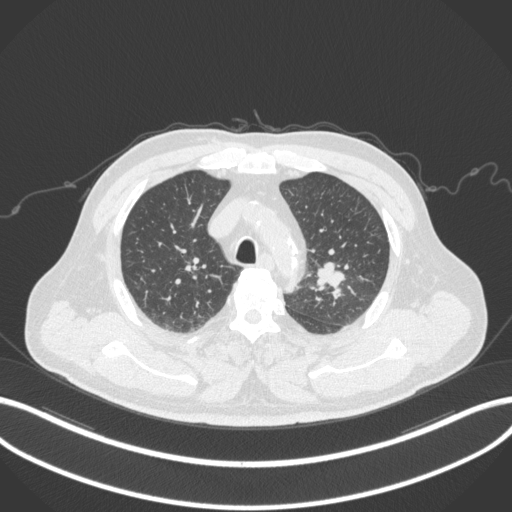
Chest CT, one axial slice; position 232 of 286 along the scan axis; reconstruction kernel B31f; 120 kVp; lung window (W 1500 / L -600 HU); 512 × 512 image matrix, field of view 400 × 400 mm. Patient: male, 67 years. From the clinical record (not read from this slice): clinical TNM (as recorded): T2a N1 M0; histopathological grade: G3.
Structures marked on this image (rectangle marked by the reading radiologist):
- lung tumour (recorded histology: adenocarcinoma): bounding box <310,256,347,295> (left, top, right, bottom; pixels)